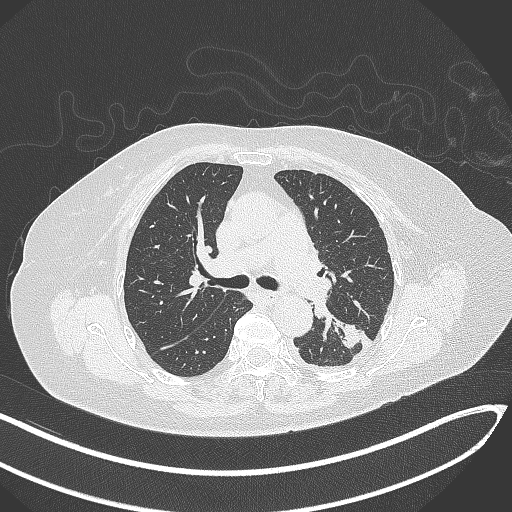
Chest CT, one axial slice; slice 199 of 270 in the series (ordered by position); reconstruction kernel B70f; lung window (W 1500 / L -600 HU); 512 × 512 image matrix, field of view 400 × 400 mm. Patient: female, 76 years. Case-level facts recorded for this patient, not image findings: clinical TNM (as recorded): T1c N0 M0.
Structures marked on this image (bounding box drawn by a radiologist):
- lung tumour (recorded histology: adenocarcinoma): bounding box (x1, y1, x2, y2) in pixels: (336, 318, 366, 350)